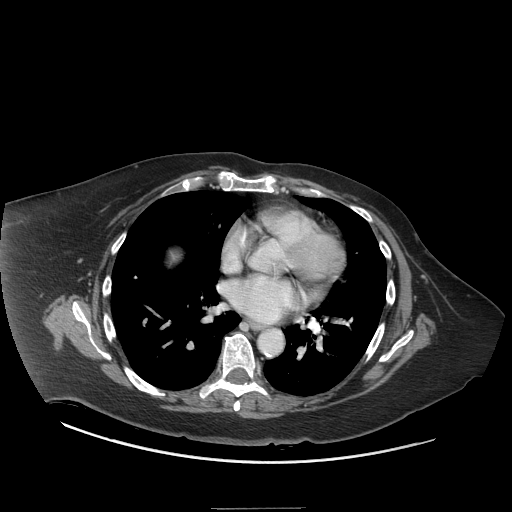
Contrast-enhanced abdominal CT (liver protocol), one axial slice; slice 78 of 81 in the series (ordered by position); reconstruction kernel STANDARD; 140 kVp; soft-tissue window (W 400 / L 40 HU); 2.5 mm slice thickness; 512 × 512 image matrix. Case-level facts recorded for this patient, not image findings: diagnosis: hepatocellular carcinoma (patient treated with transarterial chemoembolisation; whether this scan precedes or follows treatment is not stated here); TNM stage (as recorded): Stage-II; Child-Pugh class: A; tumour differentiation: moderately differentiated; tumour nodularity: multinodular.
Annotated regions visible in this slice (semi-automatic segmentation, software-assisted and operator-edited):
- liver parenchyma outside the tumour (the mass and vessels are separate outlines, so this box may not span the whole liver): bounding box [x1, y1, x2, y2] px = [170, 250, 180, 262]